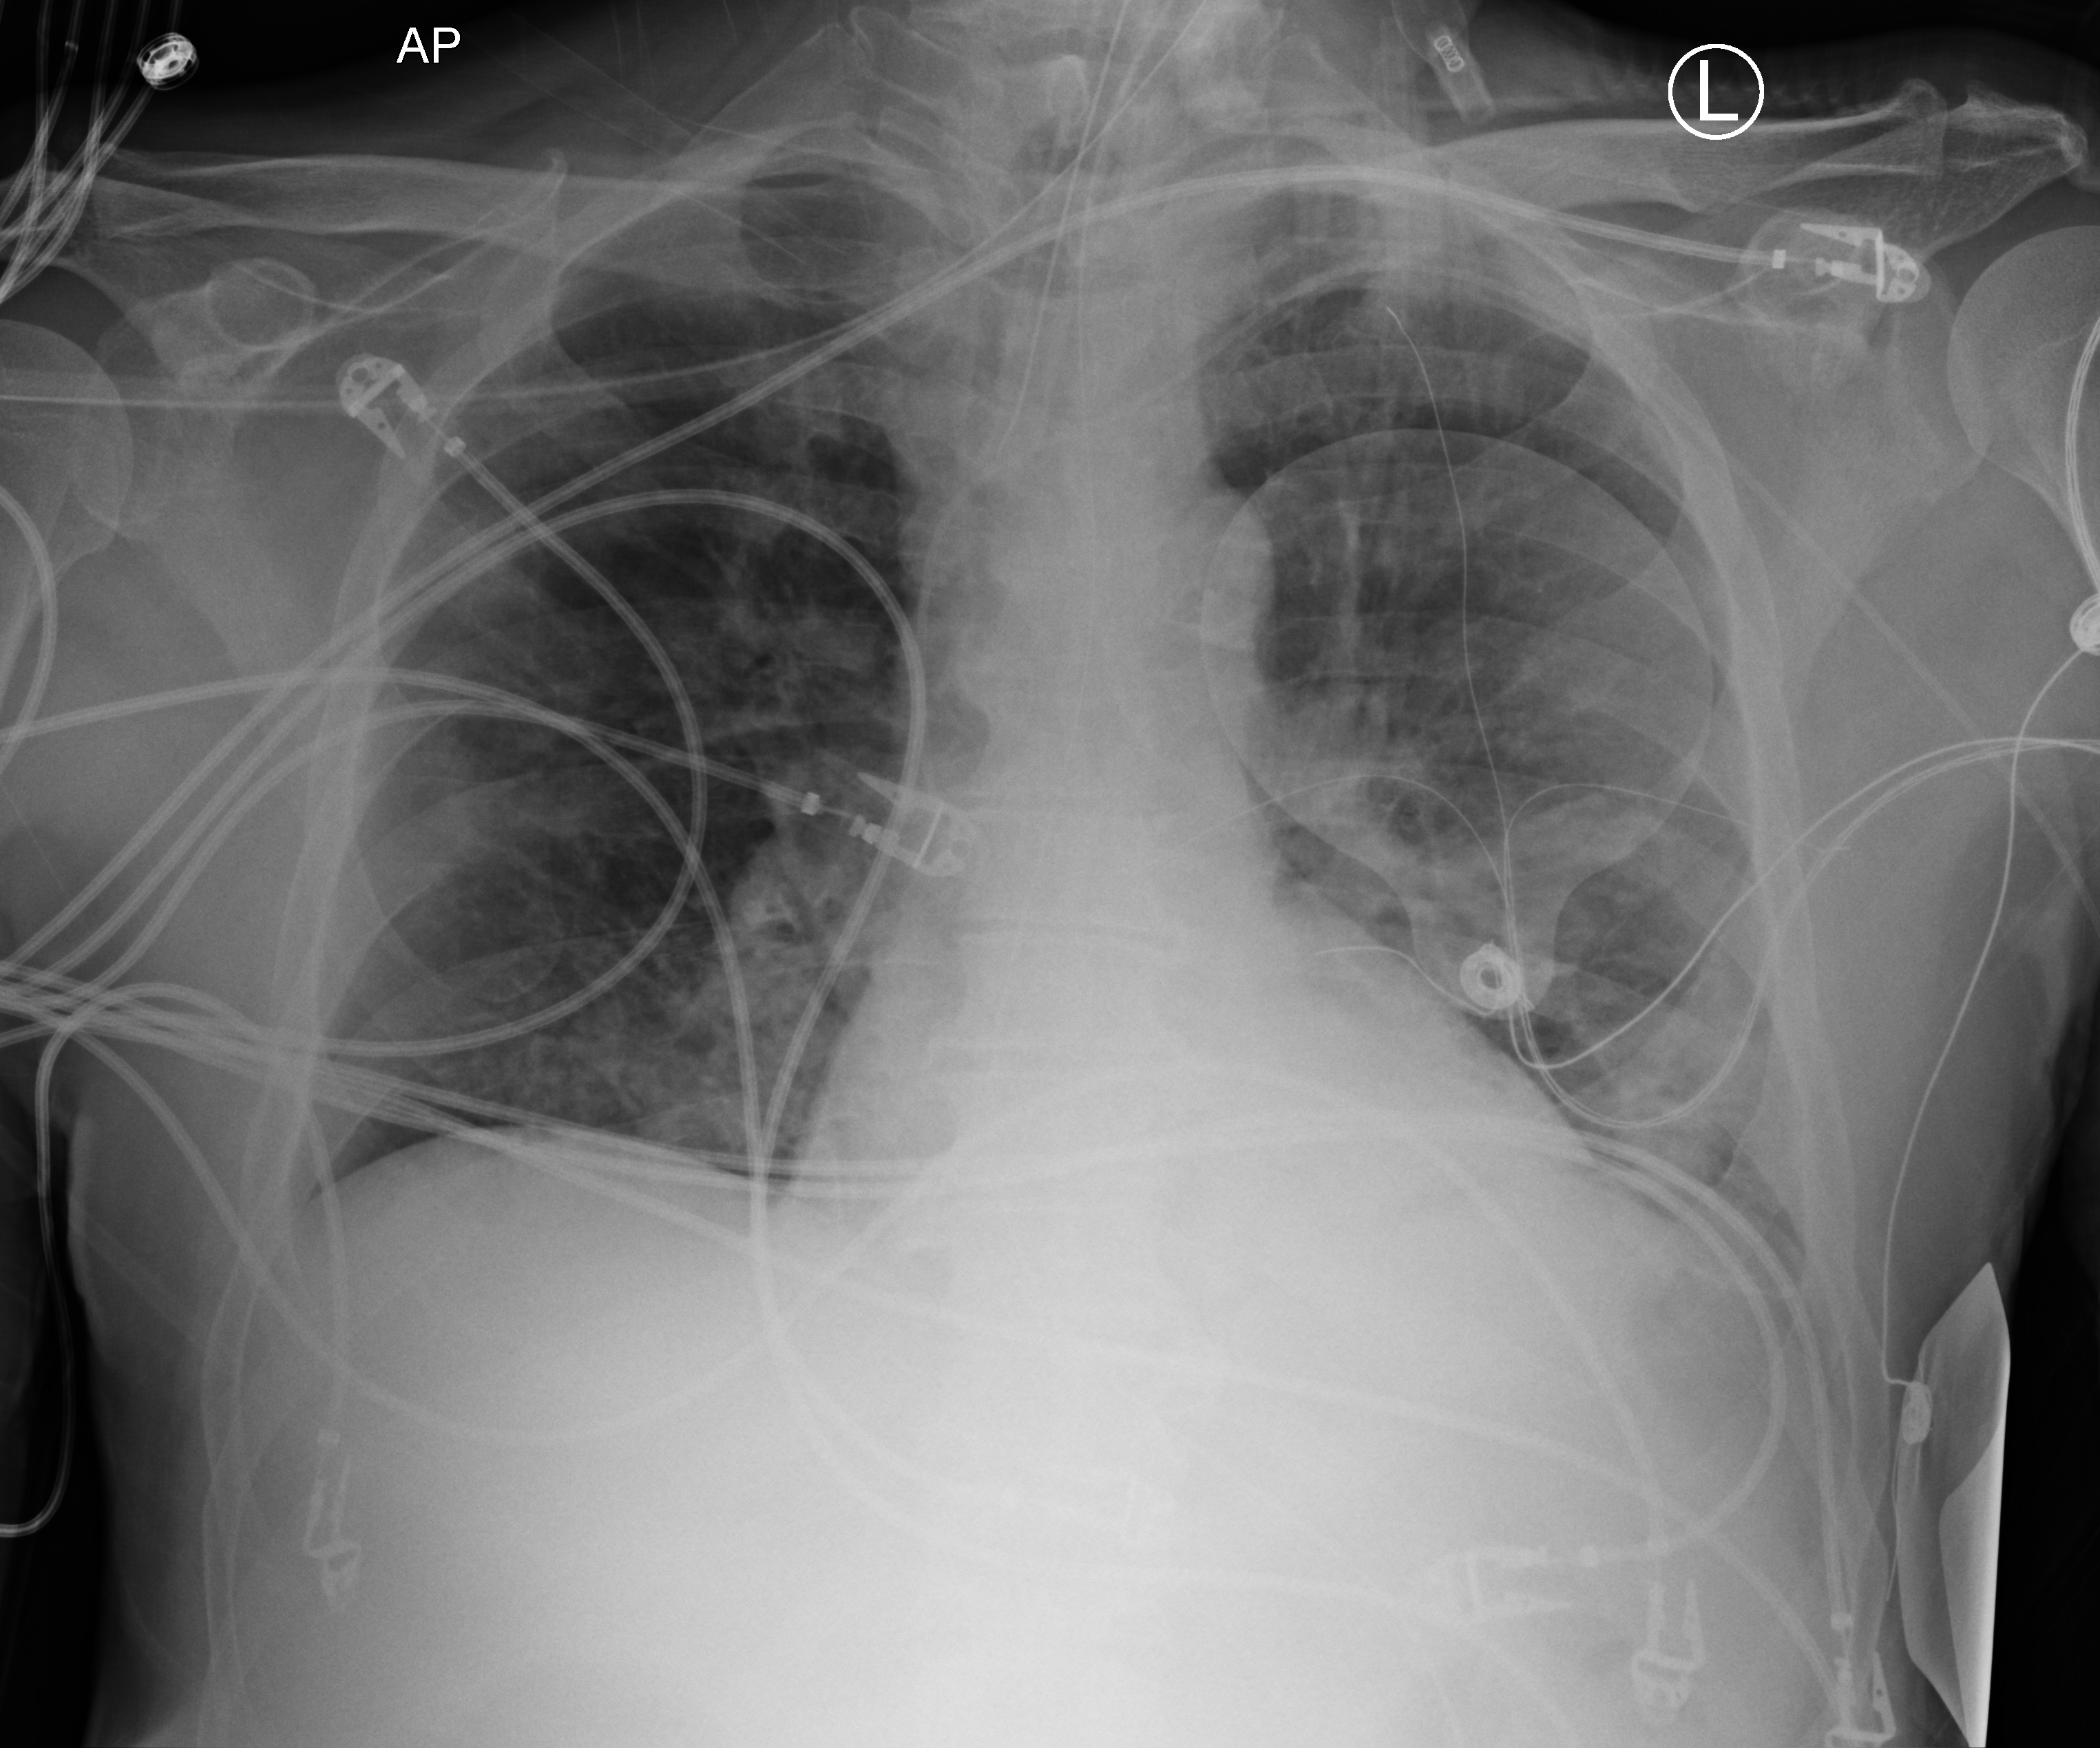
Bedside chest radiograph (computed radiography), anteroposterior (AP) projection. Patient hospitalised with COVID-19; male, aged 60–74 years.
From the hospital-stay record, not from the radiograph (when in the stay this image was taken is not recorded):
- other chronic lung disease (admission record): no
- diabetes (admission record): yes